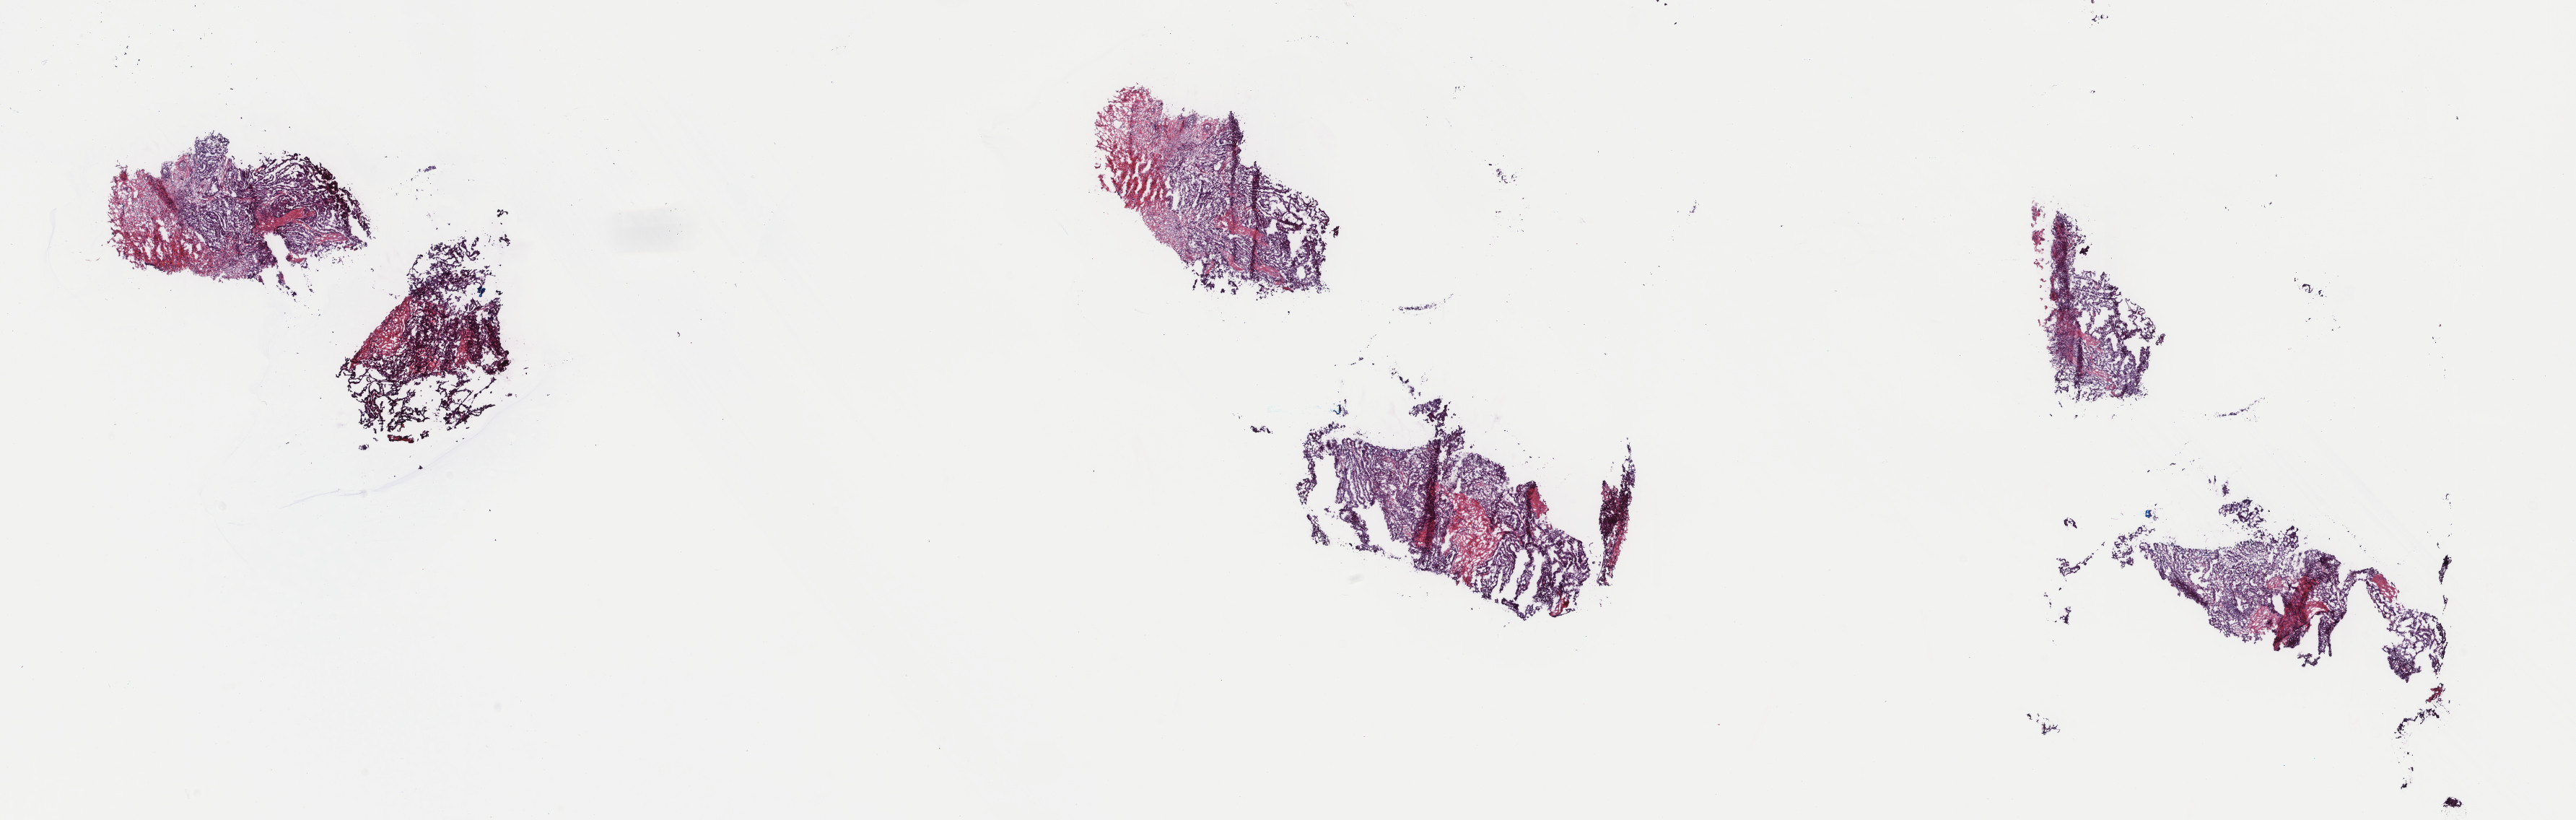
Digitized Hematoxylin and eosin (H&E) stained tissue section (whole slide), shown as a low-resolution overview of the whole scanned area (about 28.3 x 9.0 mm). Frozen section from the top of the tissue portion. Thyroid, primary tumour sample. Female, age 79 years at initial diagnosis.
Diagnosis: Papillary adenocarcinoma, NOS.